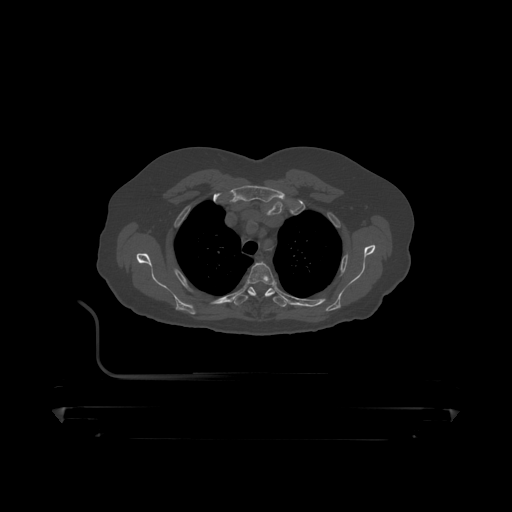
CT including the spine, one axial slice; slice 350 of 390 in the series (ordered by position); bone window (W 1800 / L 400 HU); 1.25 mm slice thickness; 512 × 512 image matrix. Male patient, age 60 years. From the clinical record (not read from this slice): primary cancer: prostate.
Outlined on this slice (semi-automatic segmentation, software-assisted and operator-edited):
- T3 vertebra: bounding box <247,263,276,287> (left, top, right, bottom; pixels)
- T4 vertebra: <234,287,287,307>